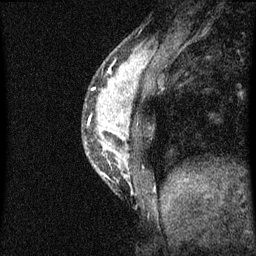
Breast MRI (dynamic contrast-enhanced), one sagittal slice; position 18 of 60 along the scan axis; dynamic contrast-enhanced series, image 2 of 3 at this slice position (ordered by acquisition); 1.5 T; TE 4.2 ms, TR 8 ms; 2 mm slice thickness; 256 × 256 image matrix. Female patient, age 33 years.
Annotated regions visible in this slice (semi-automatic segmentation, software-assisted and operator-edited):
- analysis volume of interest (the breast-tissue region the enhancement analysis was run in; not a lesion): bounding box [x1, y1, x2, y2] px = [83, 56, 151, 193]
- tumour enhancement mask (voxels above the 70 % enhancement threshold inside the analysis volume of interest): [93, 66, 130, 139]